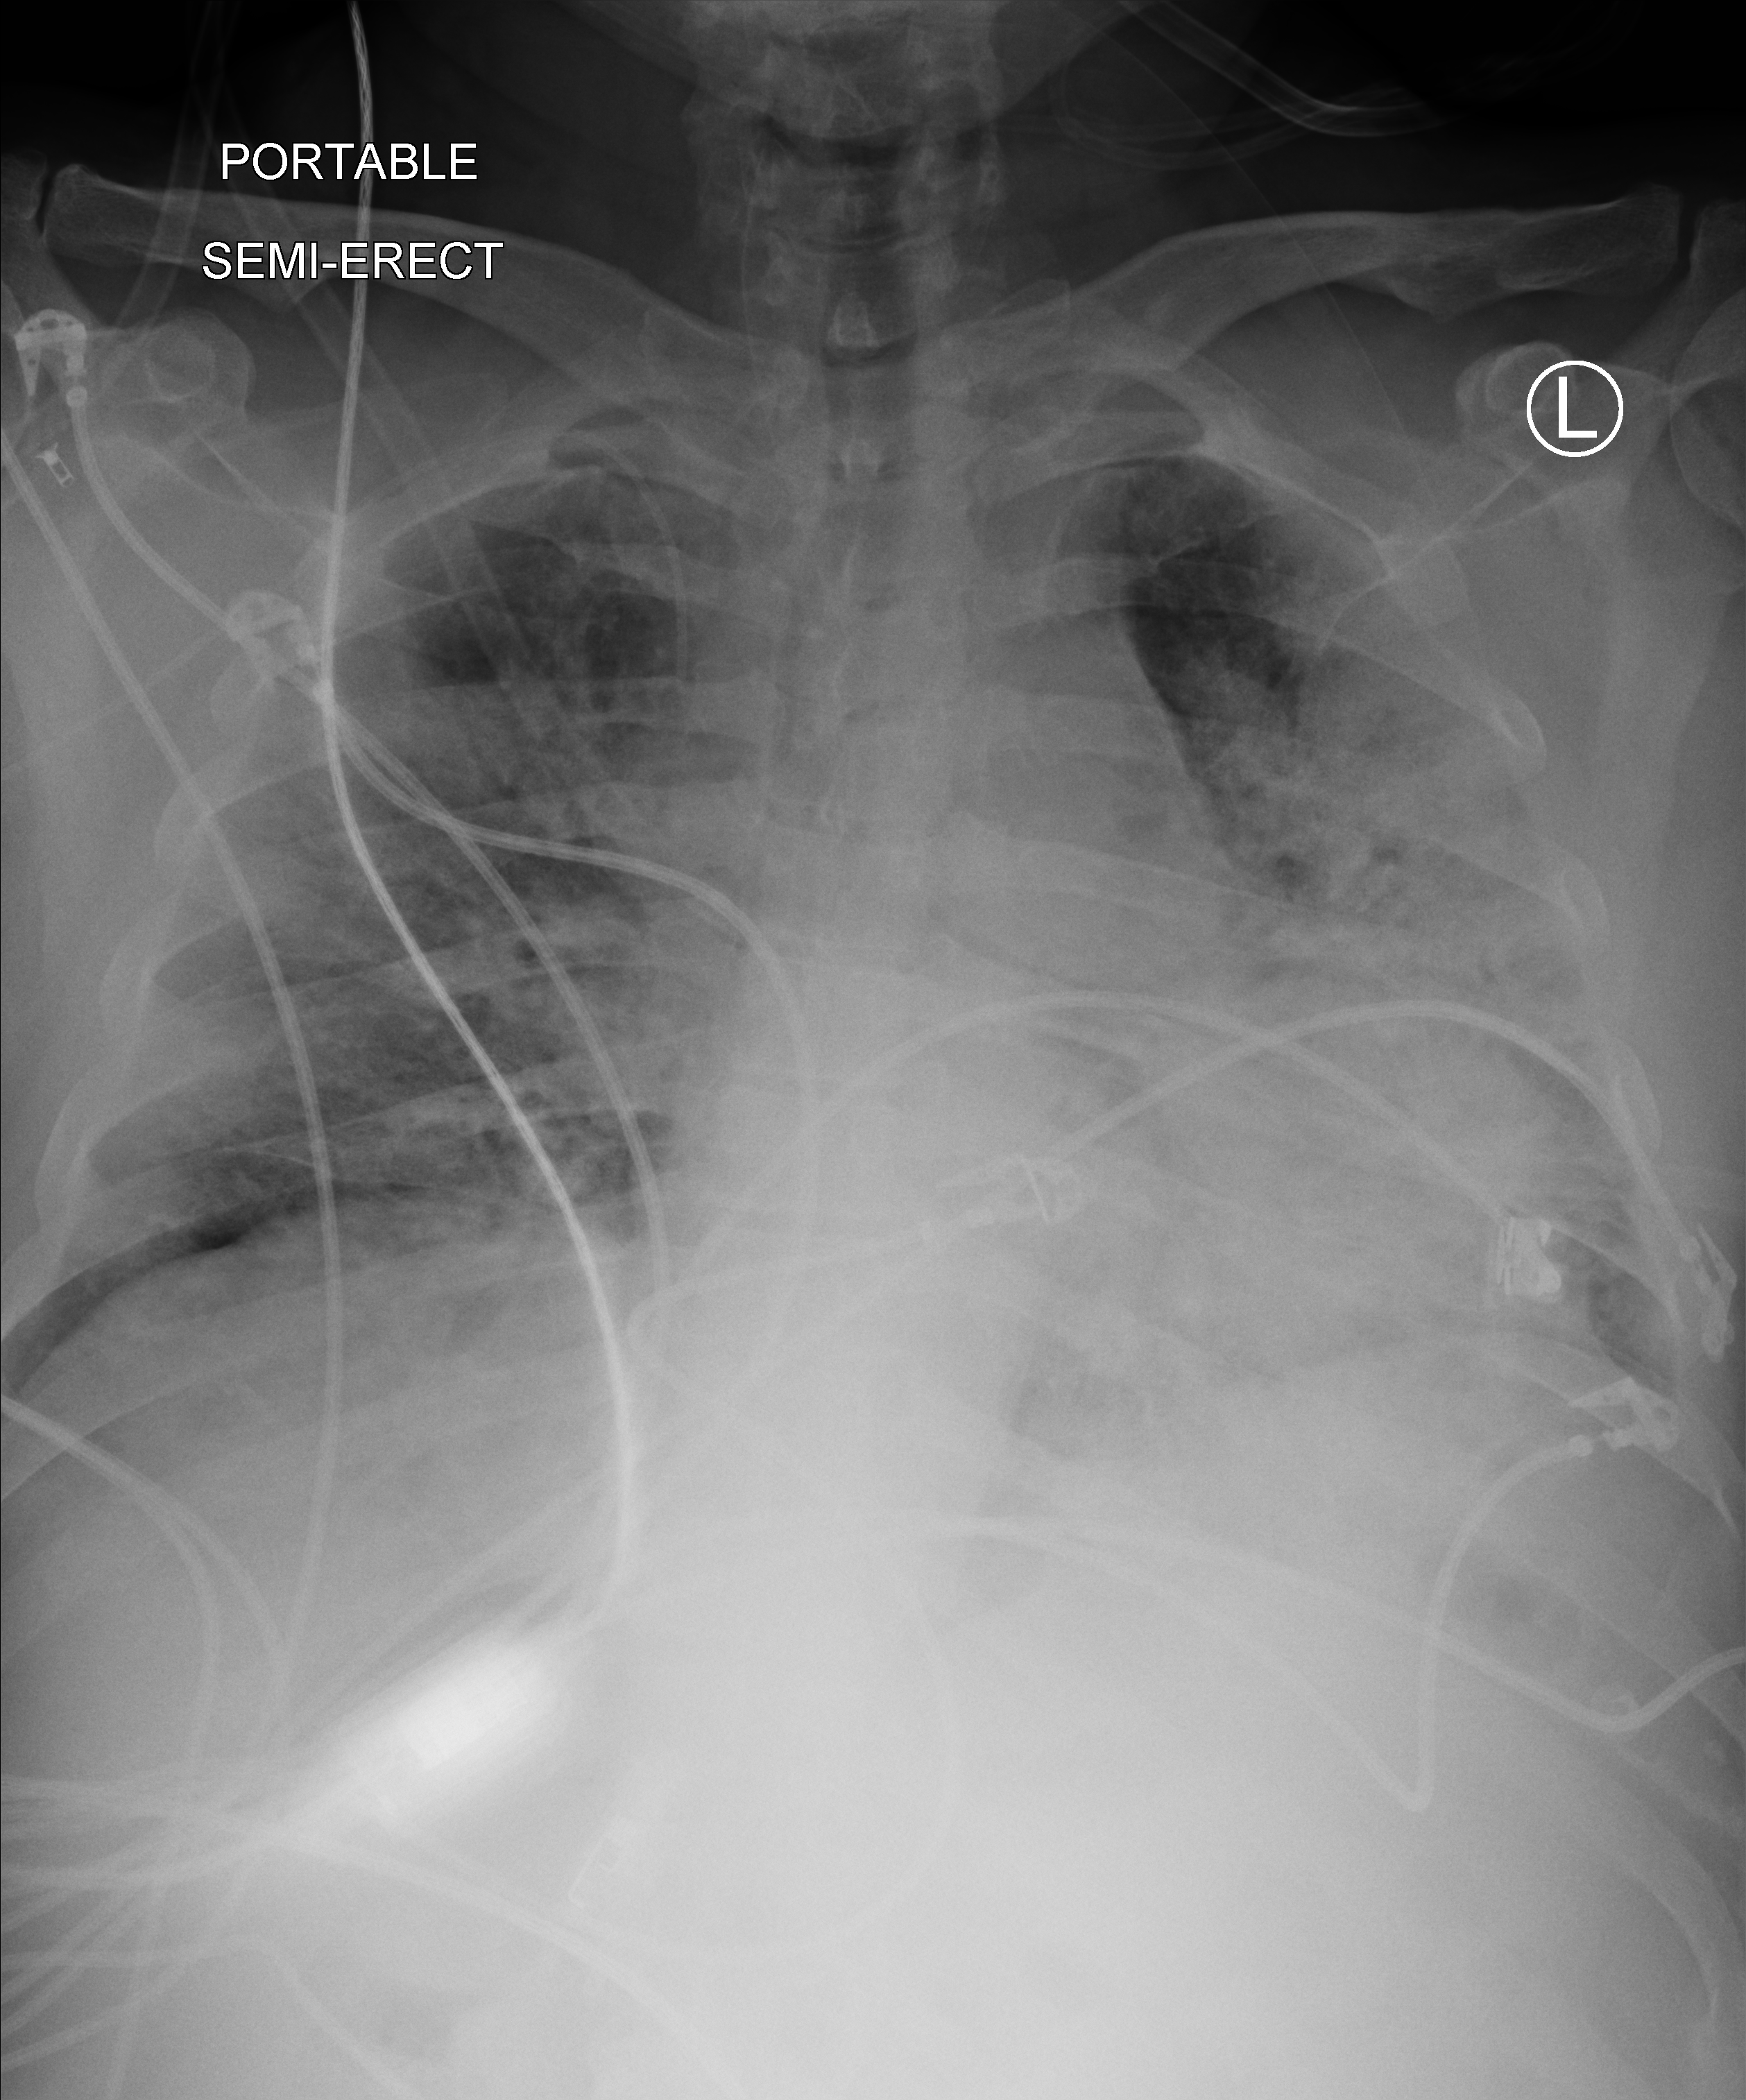
Chest X-ray (portable); anteroposterior (AP) projection. Male patient hospitalised with COVID-19, age 18–59 years.
From the hospital-stay record, not from the radiograph (when in the stay this image was taken is not recorded):
- mechanically ventilated during this hospital stay: yes
- COPD (admission record): no